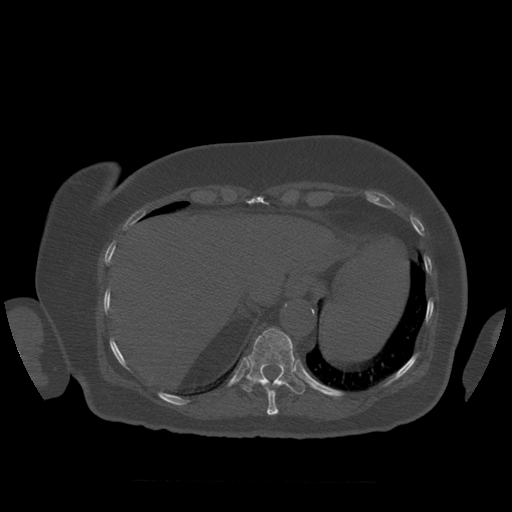
CT including the spine, one axial slice; slice 327 of 399 in the series (ordered by position); 120 kVp; bone window (W 1800 / L 400 HU); 1.25 mm slice thickness; 512 × 512 image matrix, field of view 404 × 404 mm. Patient age 81 years. From the clinical record (not read from this slice): primary cancer: renal; vertebrae with lytic lesions (as recorded): L1.
Annotated regions visible in this slice (semi-automatic segmentation, software-assisted and operator-edited):
- T10 vertebra: bounding box [x1, y1, x2, y2] px = [267, 390, 279, 416]
- T11 vertebra: [242, 328, 305, 395]